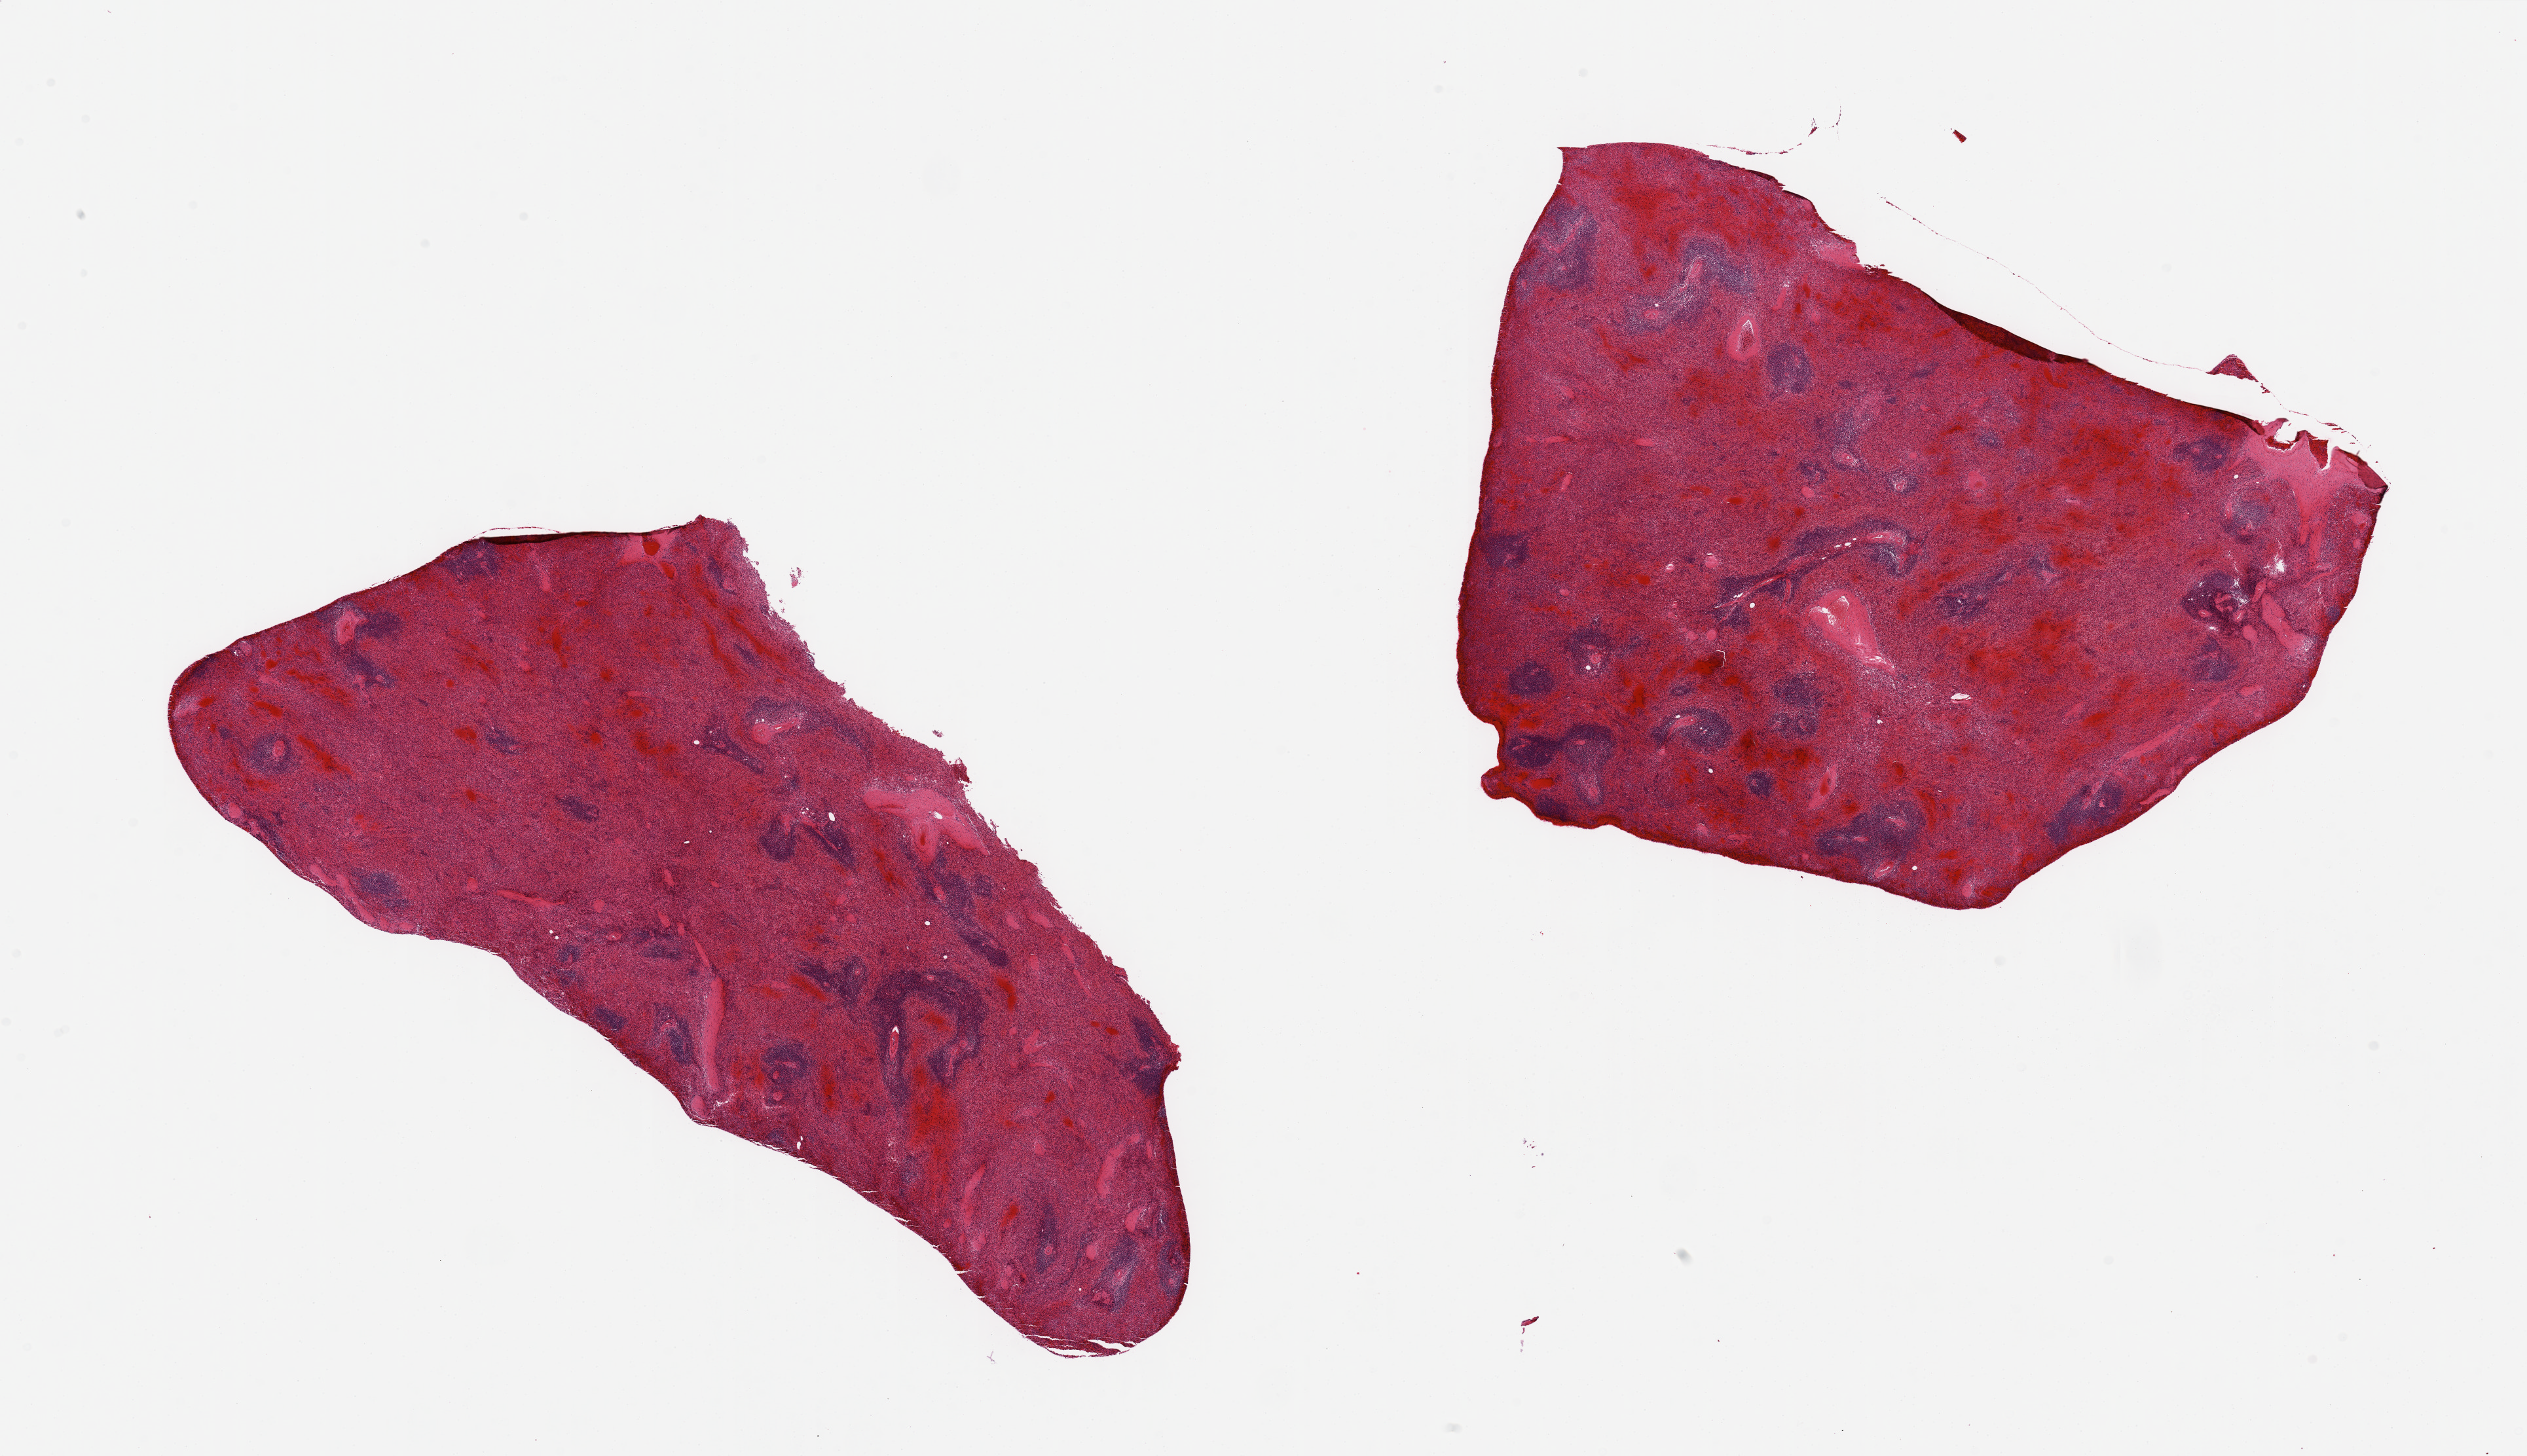
Whole-slide image, haematoxylin and eosin stain — shown as a low-resolution overview of the whole scanned area (about 30.5 x 17.6 mm, acquisition: 20x scan). PAXgene-fixed, paraffin-embedded tissue. Section of spleen (target tissue). Donor tissue sample. Donor: male.
Pathologist's review note for this sample: 2 pieces, marked congestion.